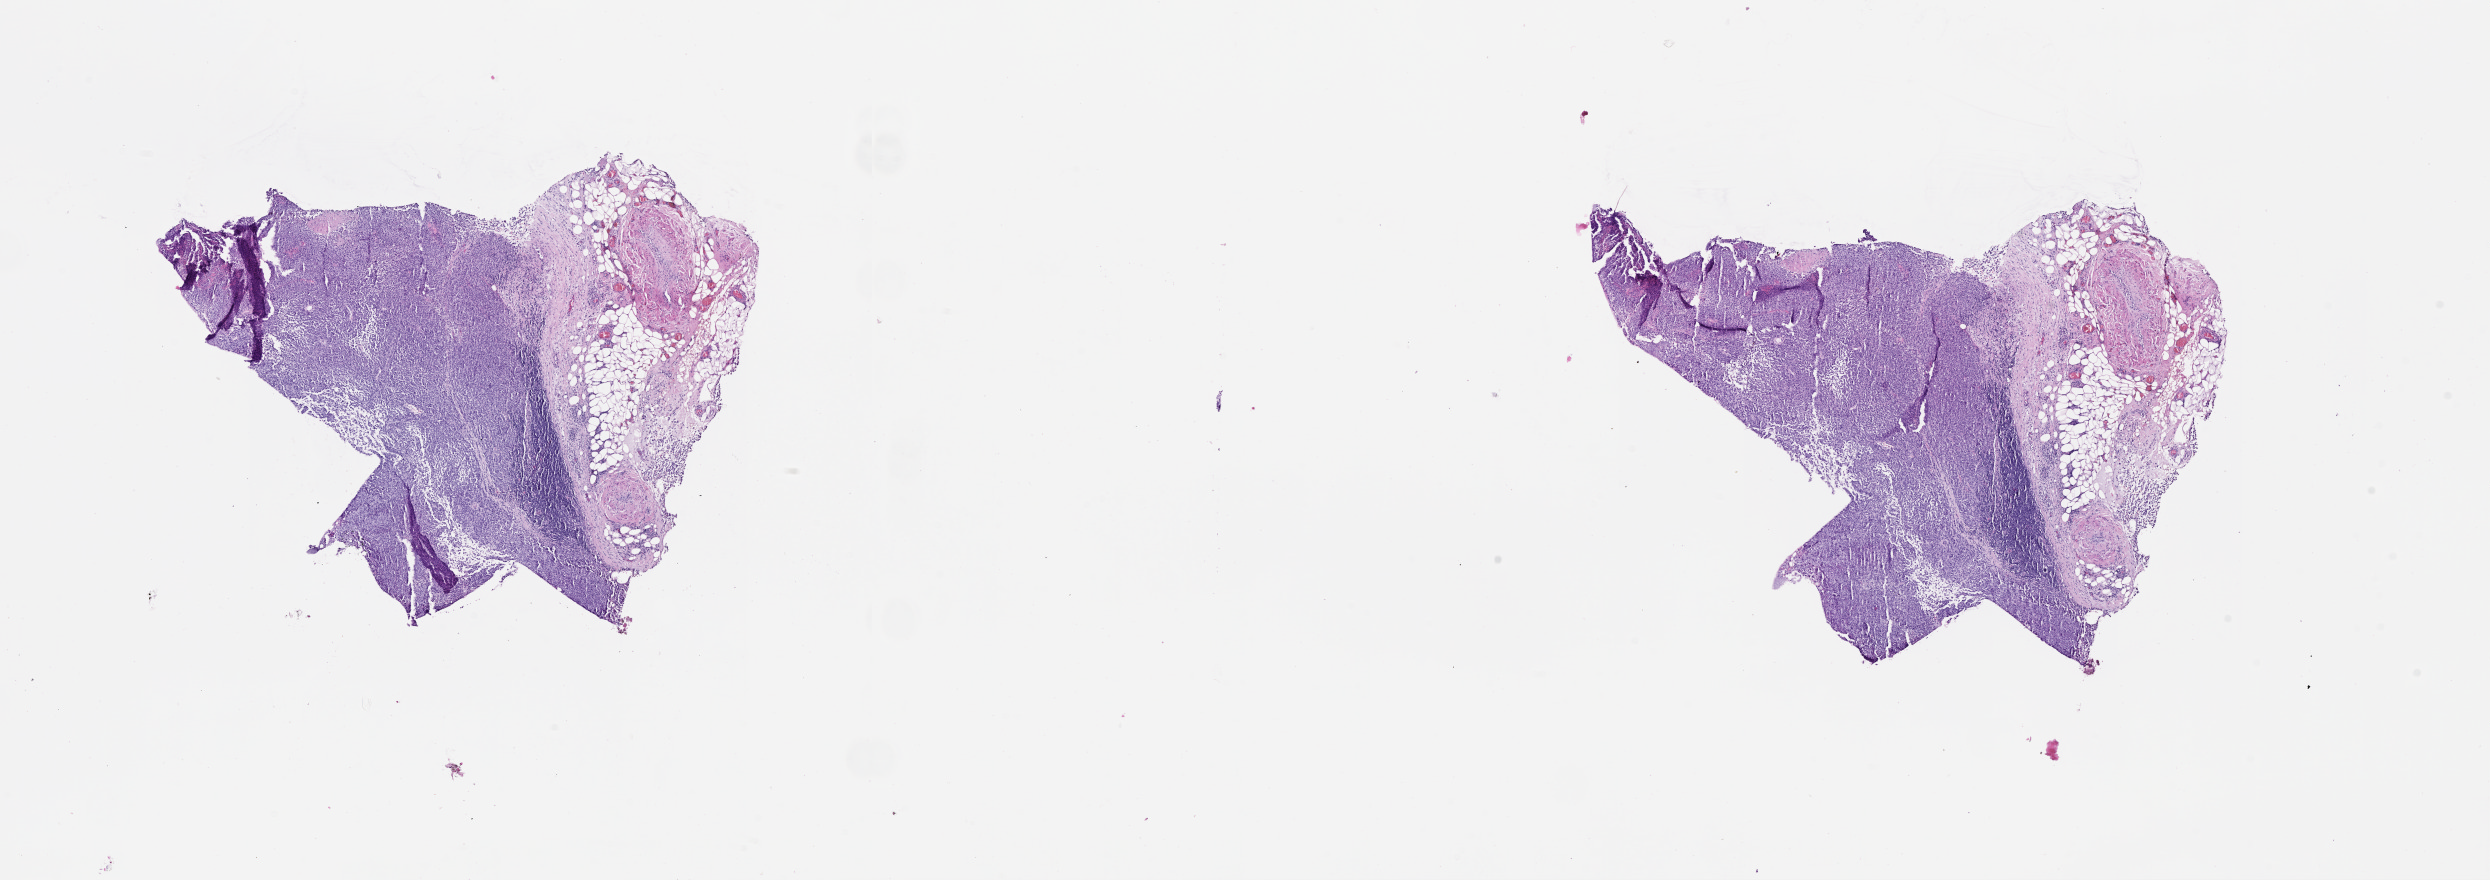
Digitized H&E-stained tissue section (whole slide), whole scanned area (about 20.0 x 7.1 mm) shown as a low-resolution overview. Male, 72 y/o.
Patient diagnosis: Malignant melanoma, NOS.